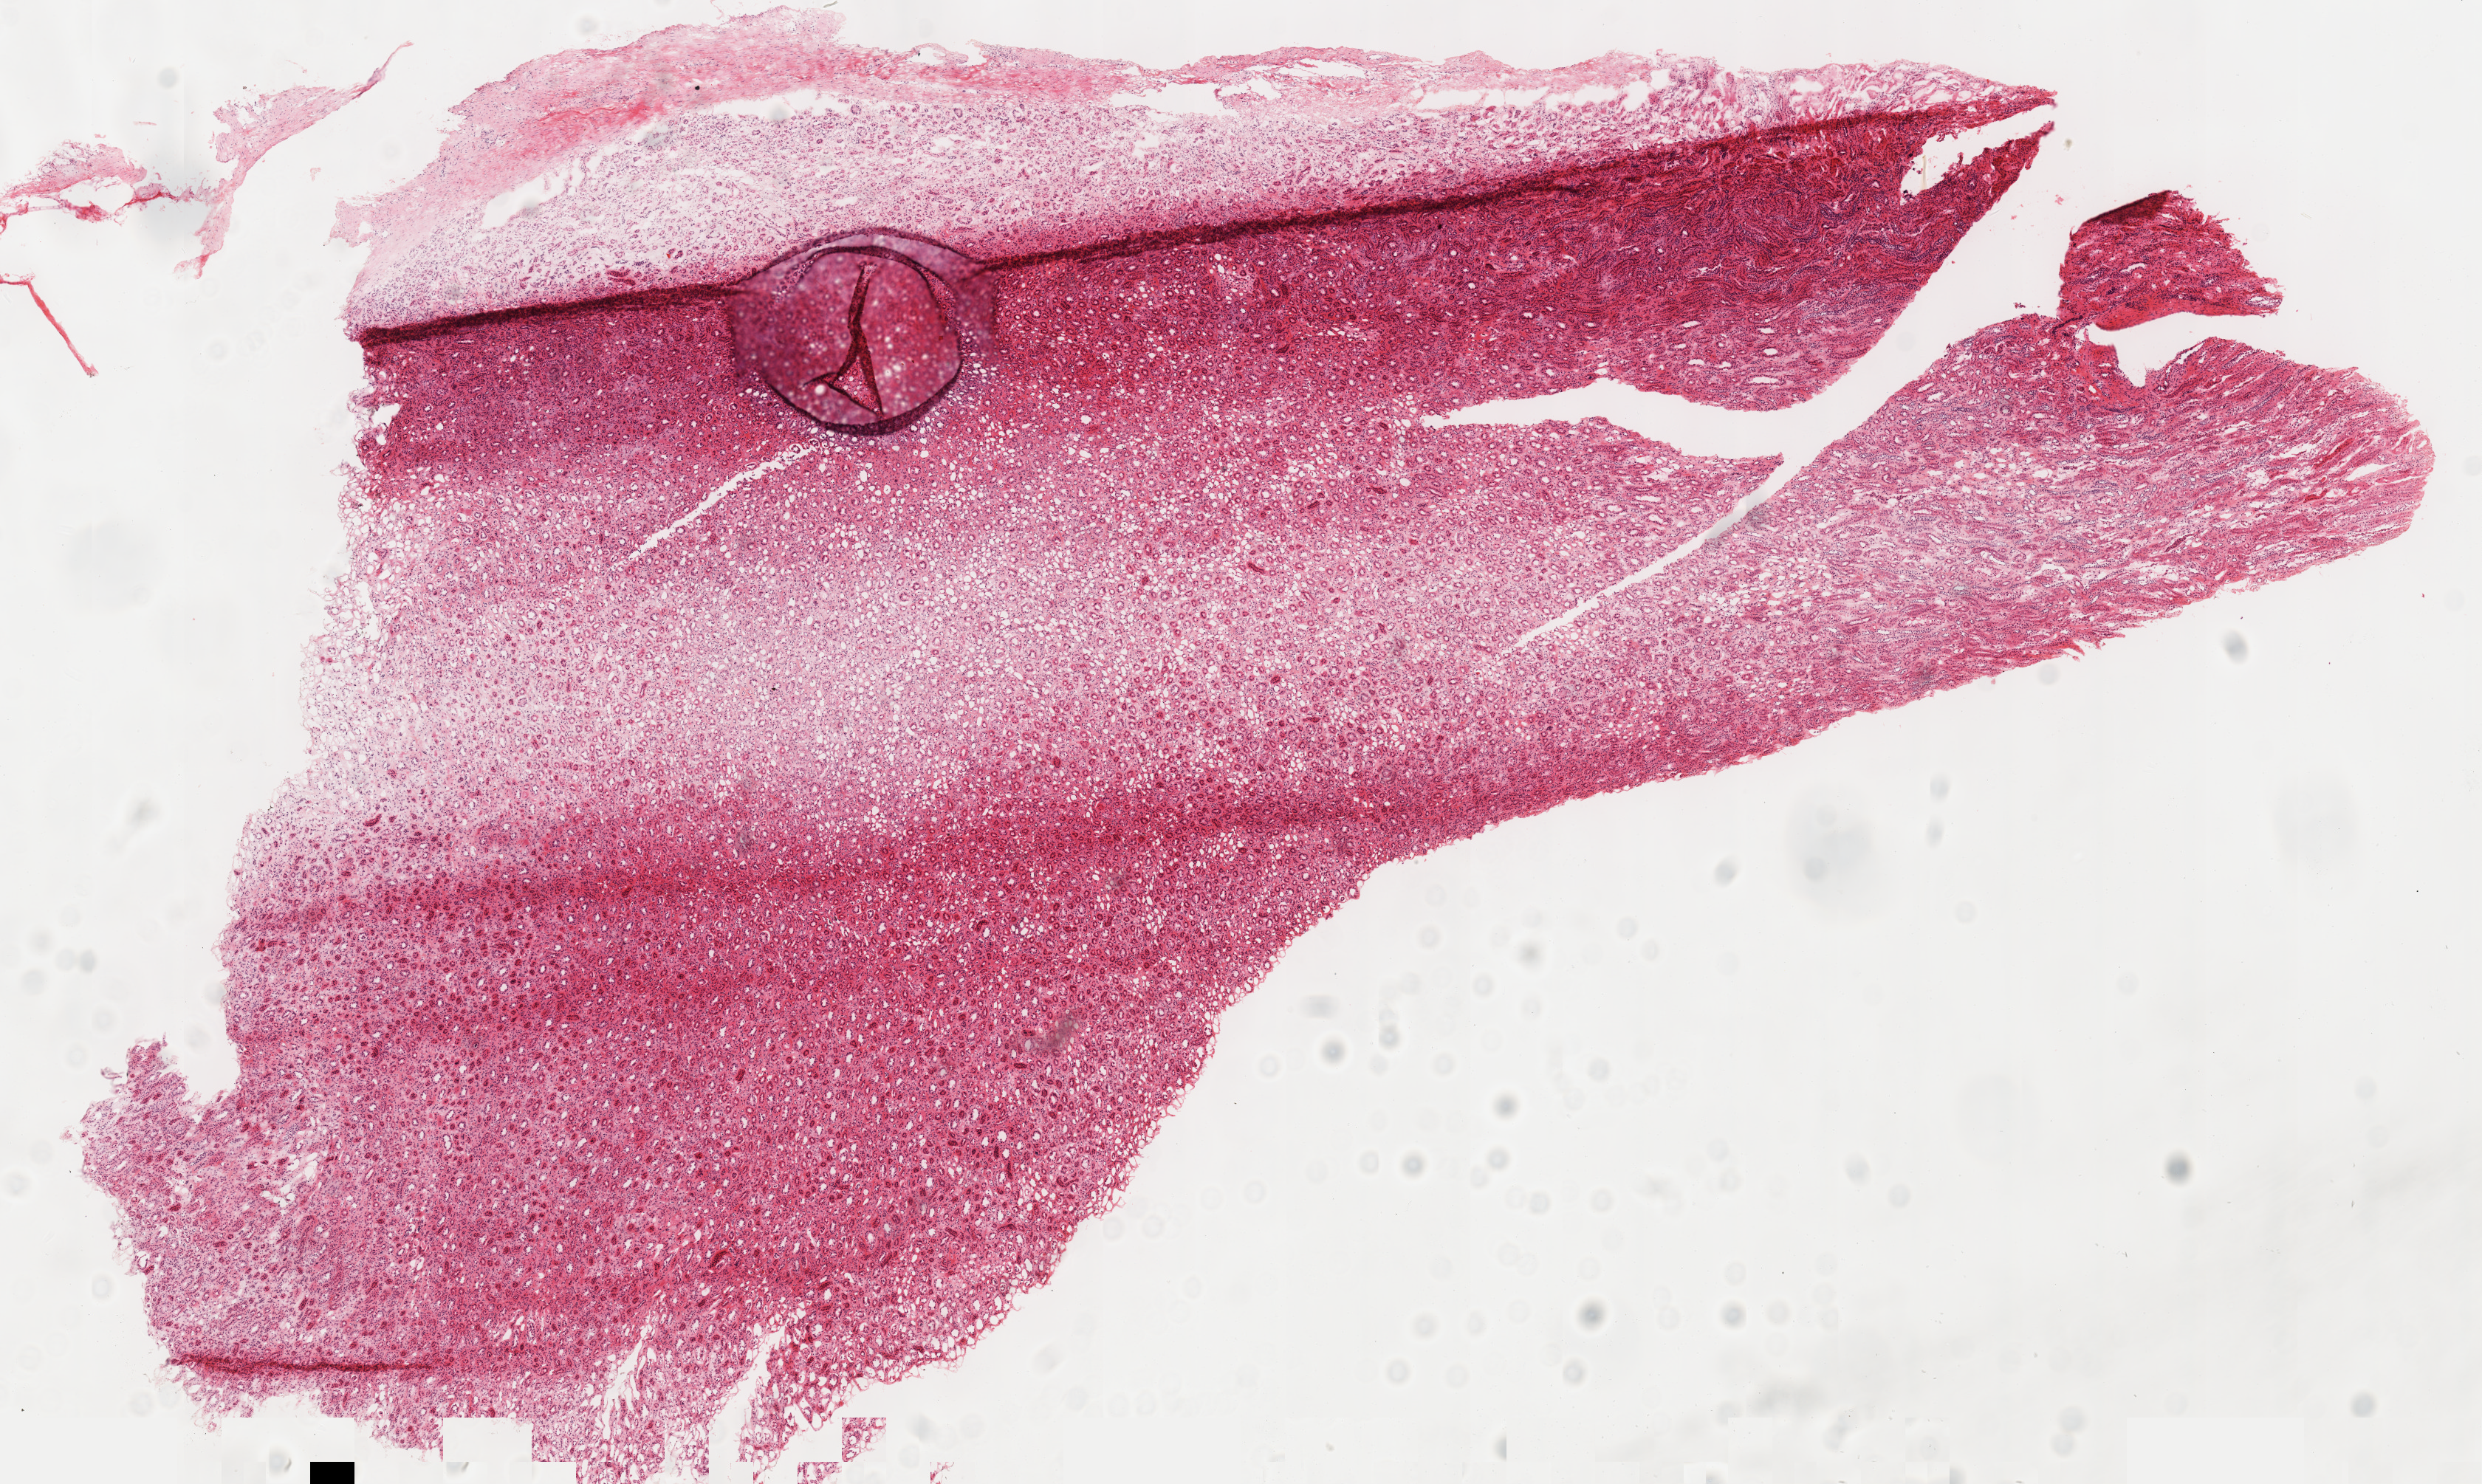
Digitized H&E tissue section (whole slide), low-resolution overview of the scanned area, about 13.2 x 7.9 mm (from a 40x scan). Frozen section from the top of the tissue portion. Sample: solid tissue normal (non-tumour tissue), kidney. Male, age 43 years at initial diagnosis. Inflammatory infiltration, as recorded: lymphocyte infiltration 2%, monocyte infiltration 0%, neutrophil infiltration 0%.
• this section: solid tissue normal sample (biorepository sample class)
• patient diagnosis: Renal cell carcinoma, chromophobe type